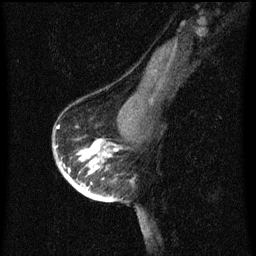
Breast MRI (dynamic contrast-enhanced), one sagittal slice. Slice 44 of 60 in the series (ordered by position). Dynamic contrast-enhanced series, image 2 of 3 at this slice position (ordered by acquisition). 1.5 T. TE 4.2 ms, TR 8 ms. 256 × 256 image matrix, field of view 180 × 180 mm. Female patient, age 56 years.
Structures marked on this image (semi-automatically segmented with operator editing):
- analysis volume of interest (the breast-tissue region the enhancement analysis was run in; not a lesion): box from (x=54, y=122) to (x=118, y=199) px
- tumour enhancement mask (voxels above the 70 % enhancement threshold inside the analysis volume of interest): (x=58, y=128)–(x=113, y=199)